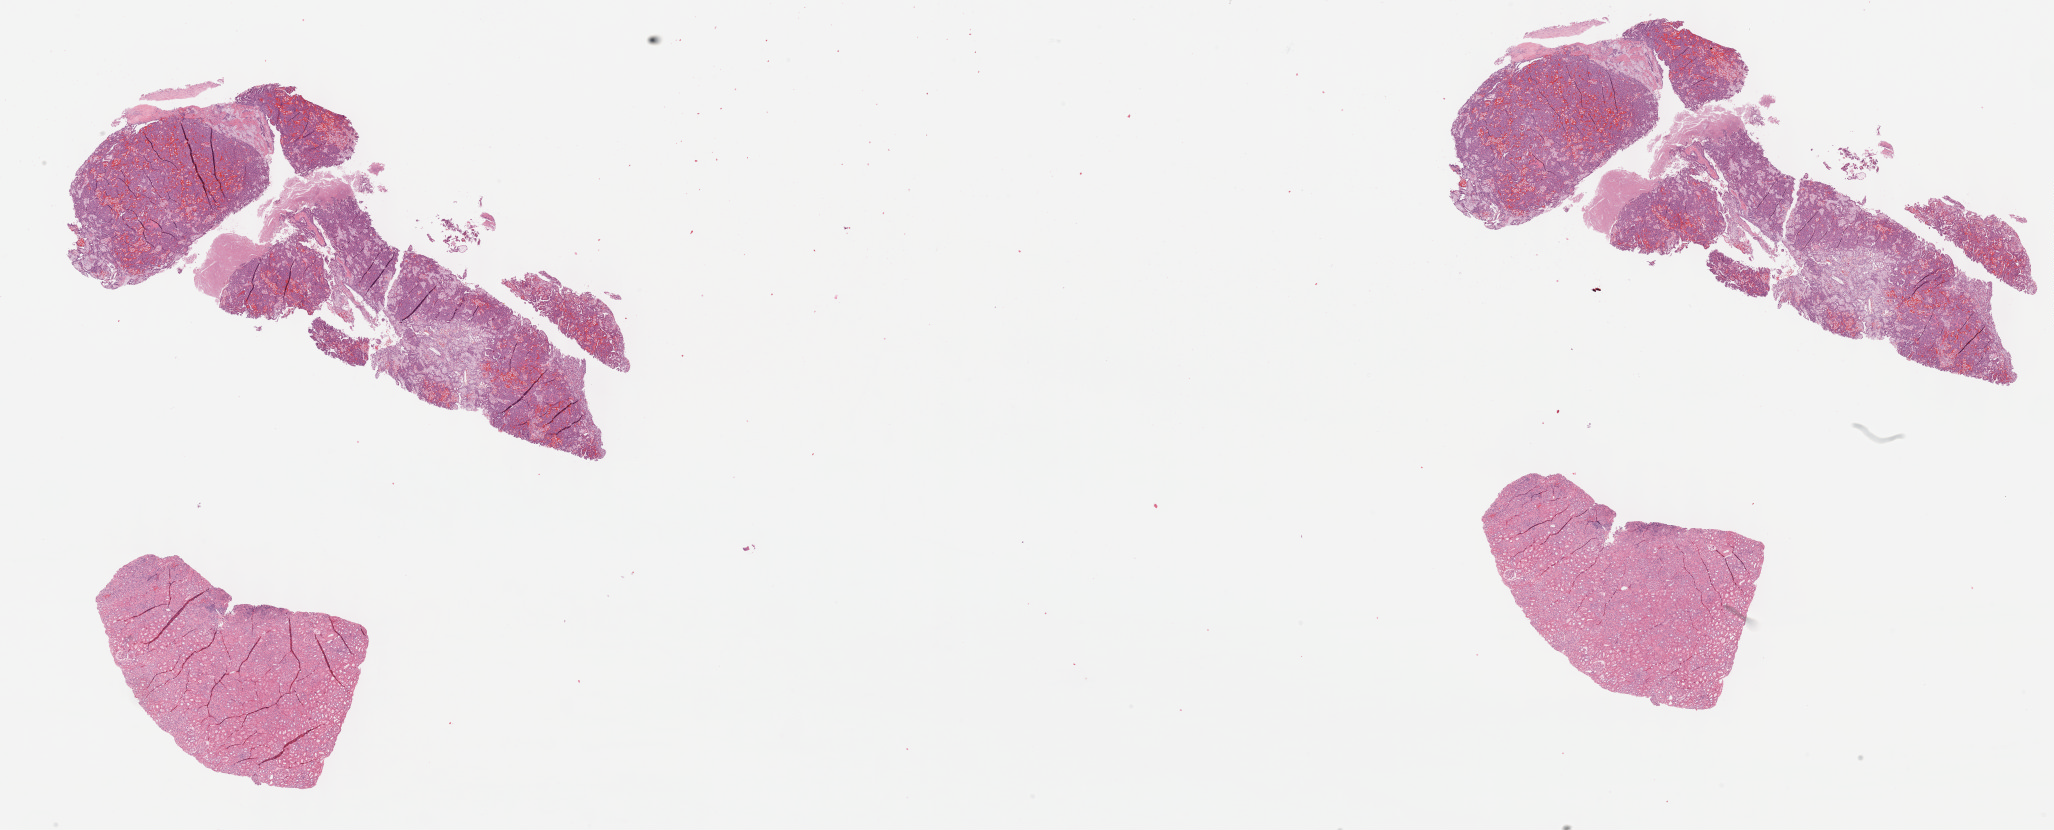
H&E-stained whole-slide image — shown as a low-resolution overview of the whole scanned area (about 33.2 x 13.4 mm); formalin-fixed paraffin-embedded (FFPE) diagnostic section; primary tumour sample from the kidney. Male patient; age at initial diagnosis 66 years.
AJCC pathologic stage: II (7th edition). Diagnosis: Papillary adenocarcinoma, NOS.